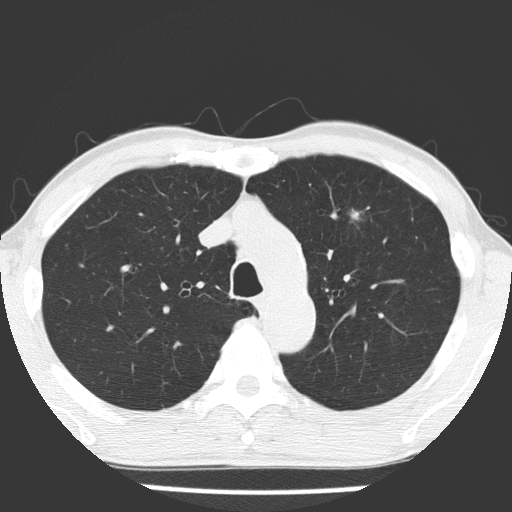
Chest CT (low-dose screening protocol), one axial image, first (baseline) screen, lung window (W 1500 / L -600 HU), 2 mm slice thickness, slice 52 of 177 in the series, 512 × 512 image matrix. Male participant, aged 66 years at enrolment. Current smoker at enrolment.
Expert reader's lesion annotation, bounding box (x1, y1, x2, y2) in pixels: (329, 195, 377, 240). Reader record for this screening exam (exam-level; its link to the box is not recorded): non-calcified nodule or mass ≥4 mm, left upper lobe, 8 × 8 mm, poorly defined margins, mixed attenuation. Official screen result: positive, change unspecified: nodule(s) >= 4 mm or enlarging nodule(s), mass(es), or other non-specific abnormalities suspicious for lung cancer.